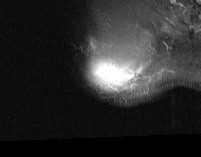
MRI of an extremity soft-tissue mass, one axial slice. Slice 59 of 74 in the series (ordered by position). STIR. MR volume resampled by the dataset authors to the PET/CT grid (not the native acquisition matrix). 3.27 mm slice thickness. 201 × 157 image matrix. Male patient. Case-level facts recorded for this patient, not image findings: histological type: pleiomorphic spindle cell undifferentiated; grade: high; site of the primary tumour: right parascapusular.
Outlined on this slice (expert contour drawn on MRI and transferred to this co-registered scan by the dataset authors):
- gross tumour volume including surrounding oedema: bounding box [x1, y1, x2, y2] px = [95, 59, 143, 85]
- gross tumour volume (mass): [97, 59, 116, 81]